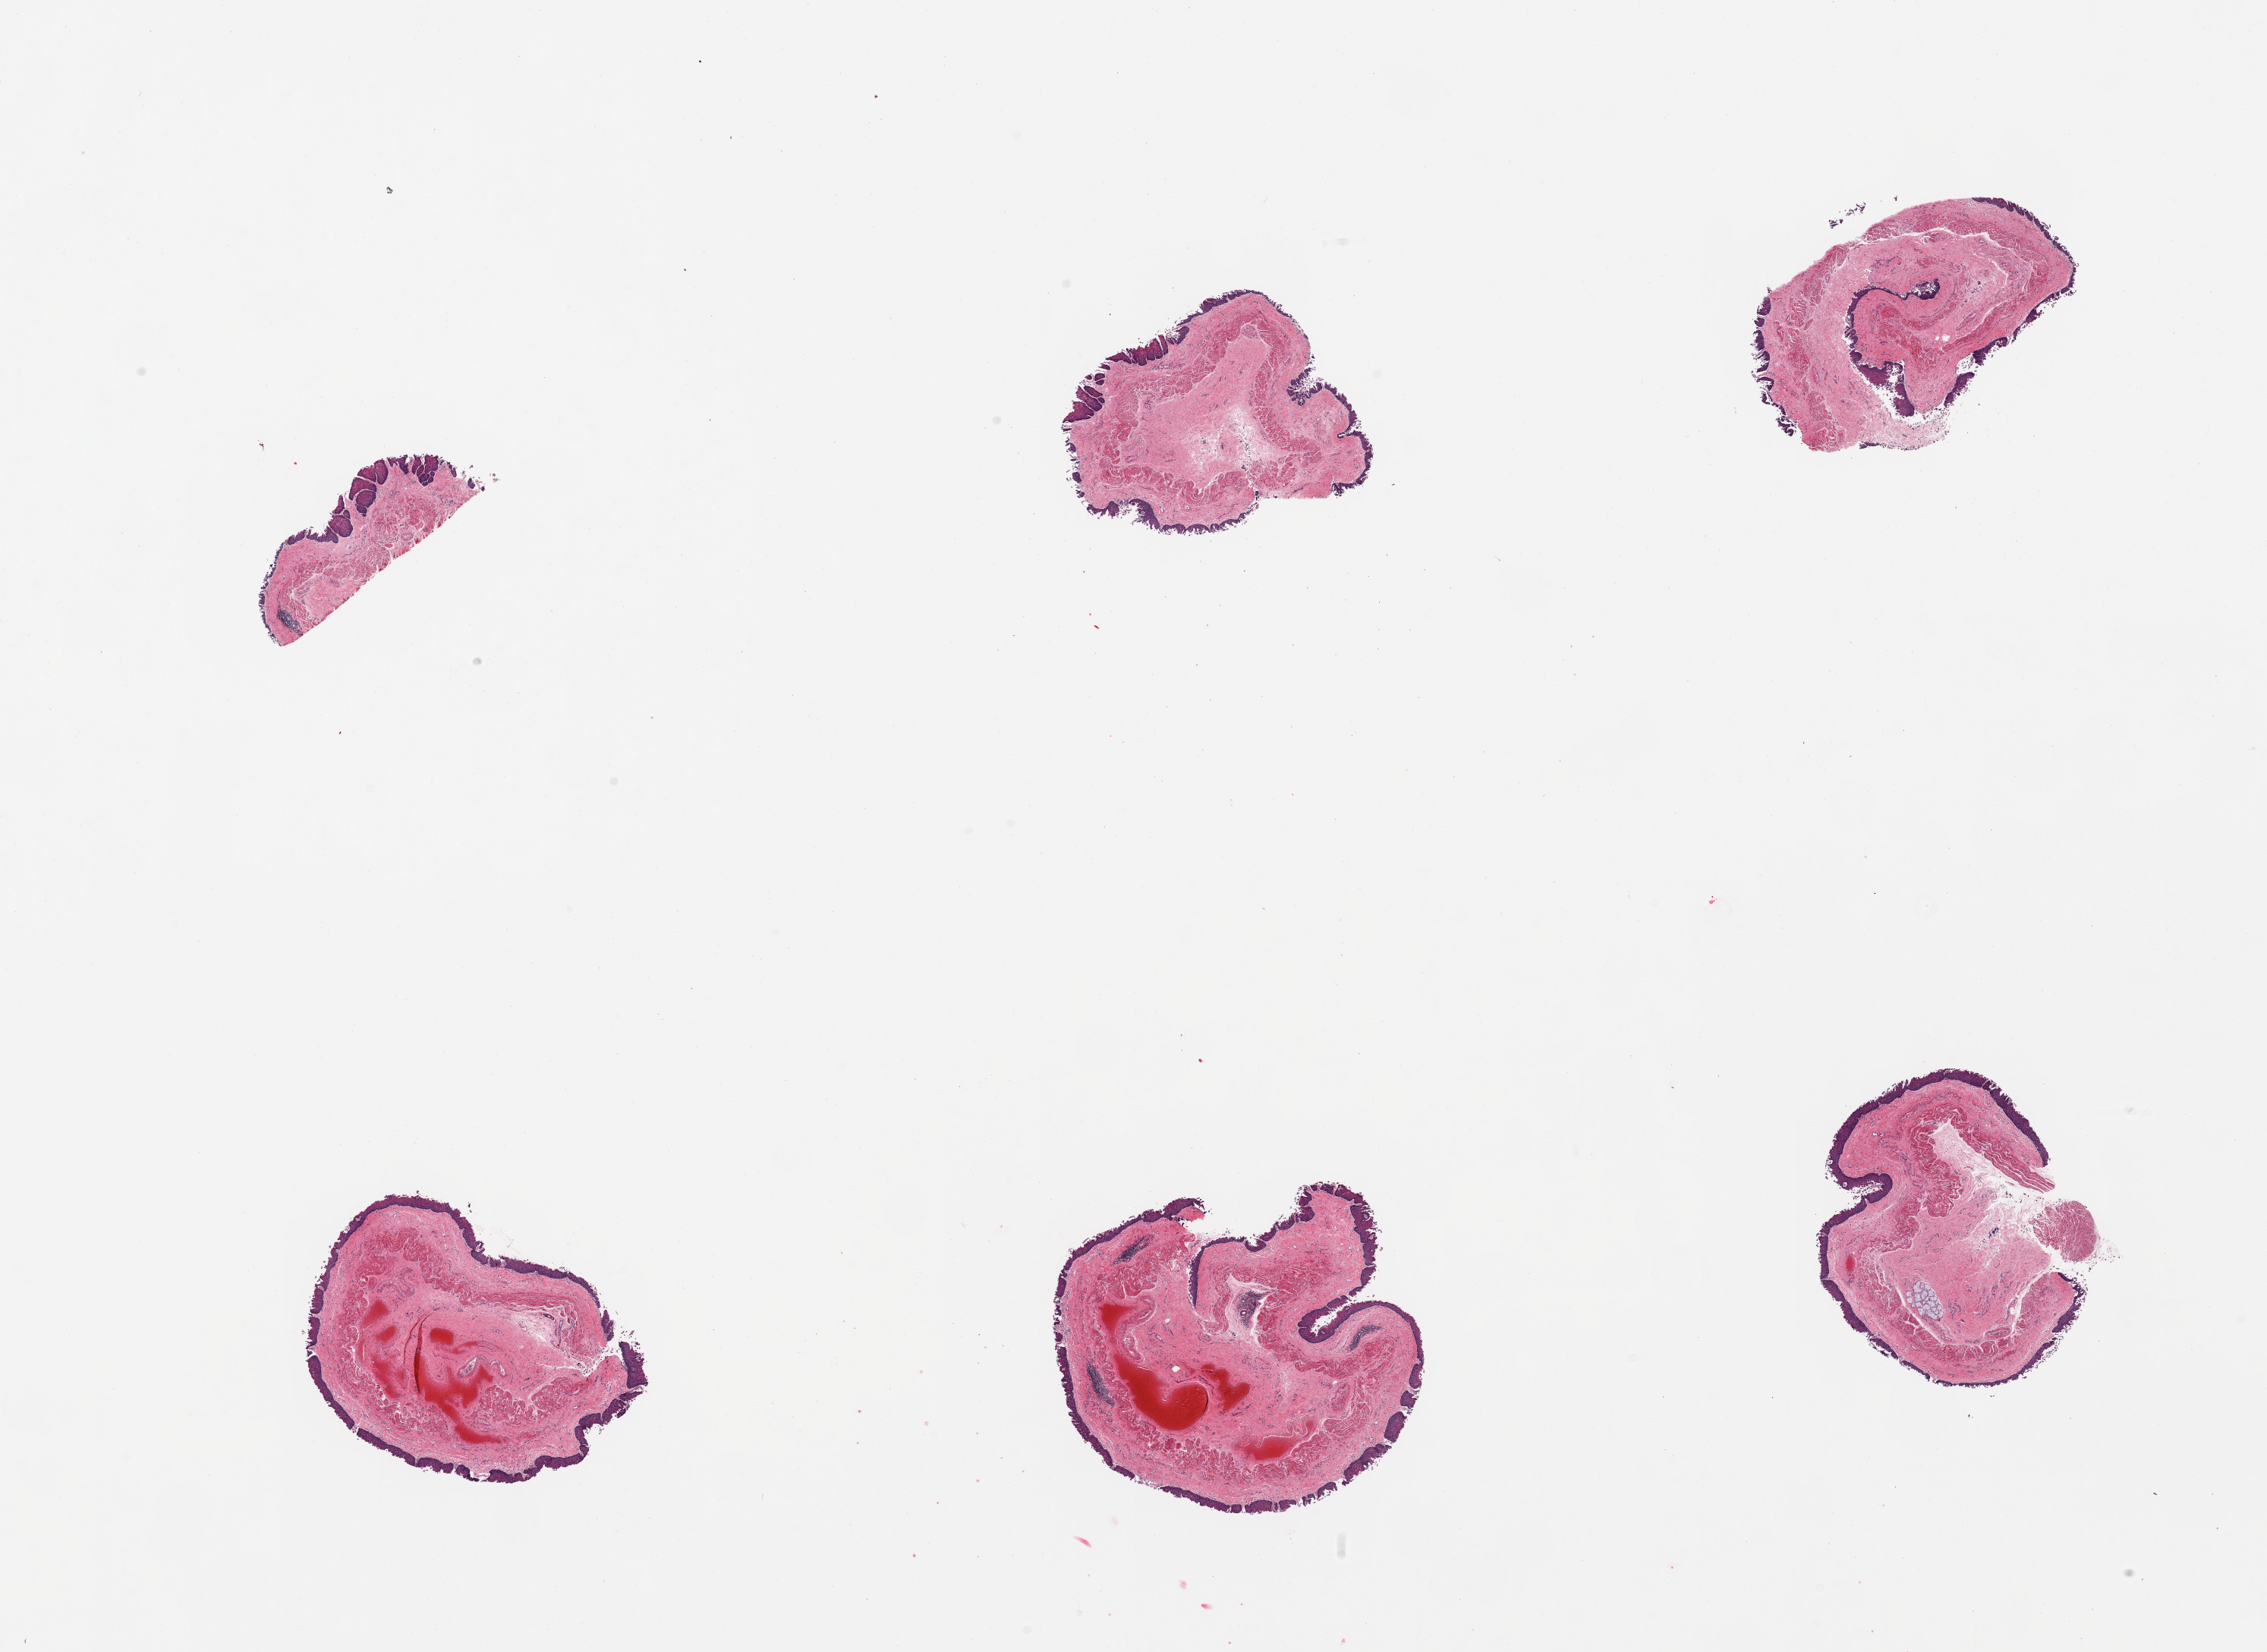
Digitized hematoxylin and eosin (H&E)-stained section, low-resolution overview of the scanned area, about 23.6 x 17.2 mm. PAXgene-fixed paraffin-embedded (PFPE) section. Target tissue: esophageal mucous membrane. Donor tissue sample. Donor: male.
- pathologist's review note for this sample: 6 pieces; moderate sloughing of epithelium